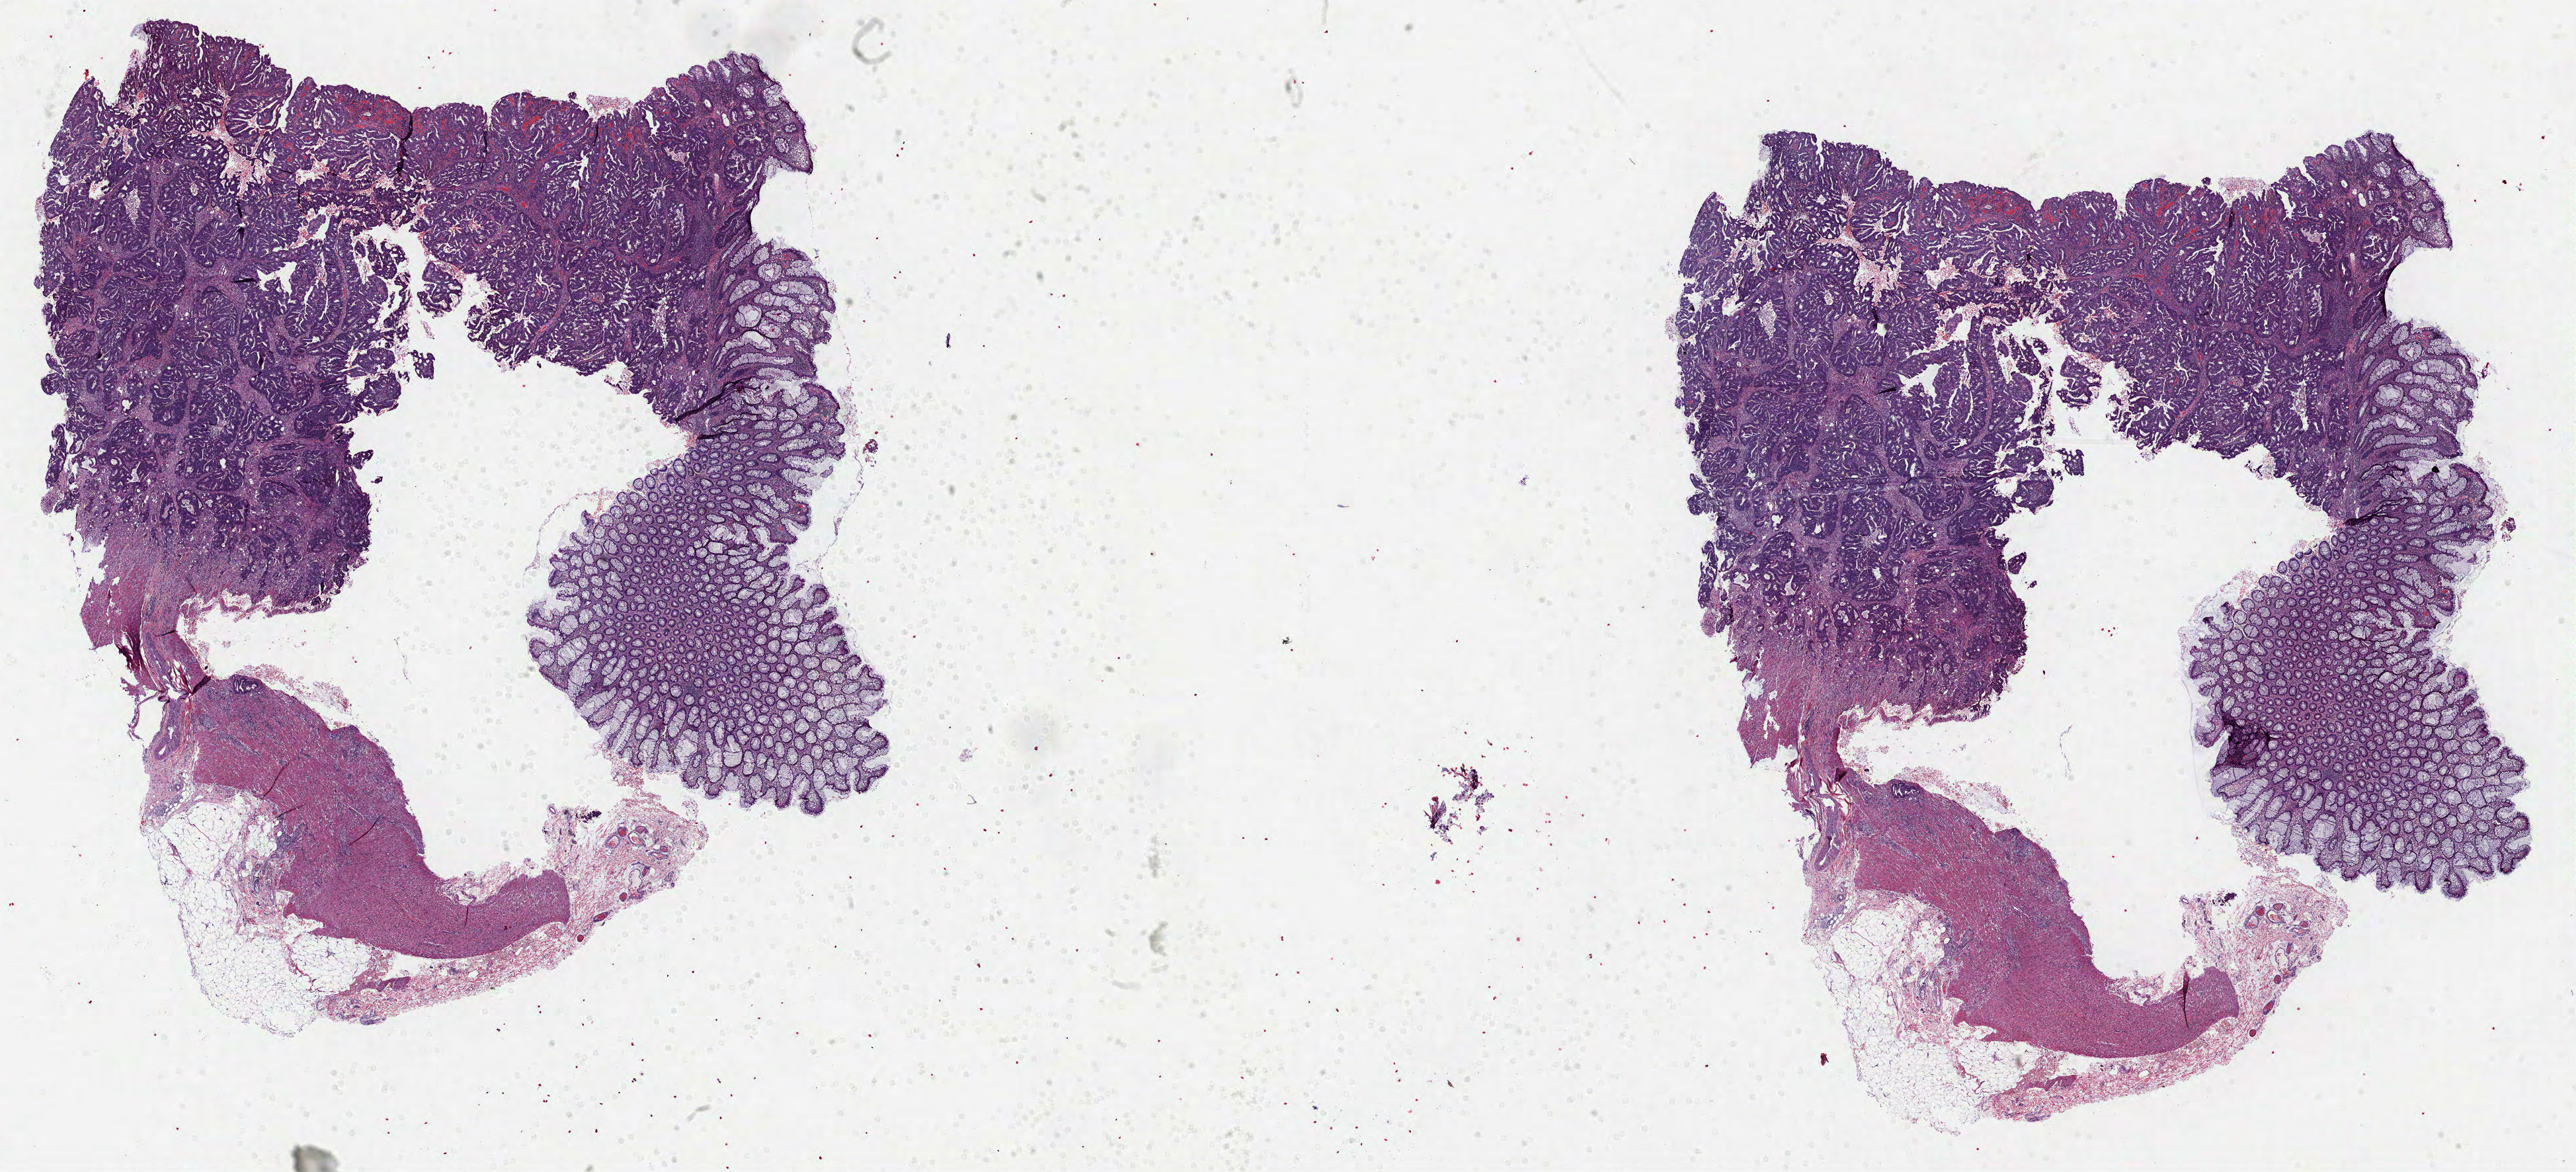
H&E-stained whole-slide image — low-resolution overview of the scanned area, about 31.4 x 14.3 mm, formalin-fixed paraffin-embedded (FFPE) diagnostic section, primary tumour sample from the colon. Female patient; age at initial diagnosis 48 years.
Diagnosis: Adenocarcinoma, NOS. TNM: T3 N0 M0. Lymph nodes positive (case pathology): 0 of 29 examined. AJCC pathologic stage: IIA (6th edition).